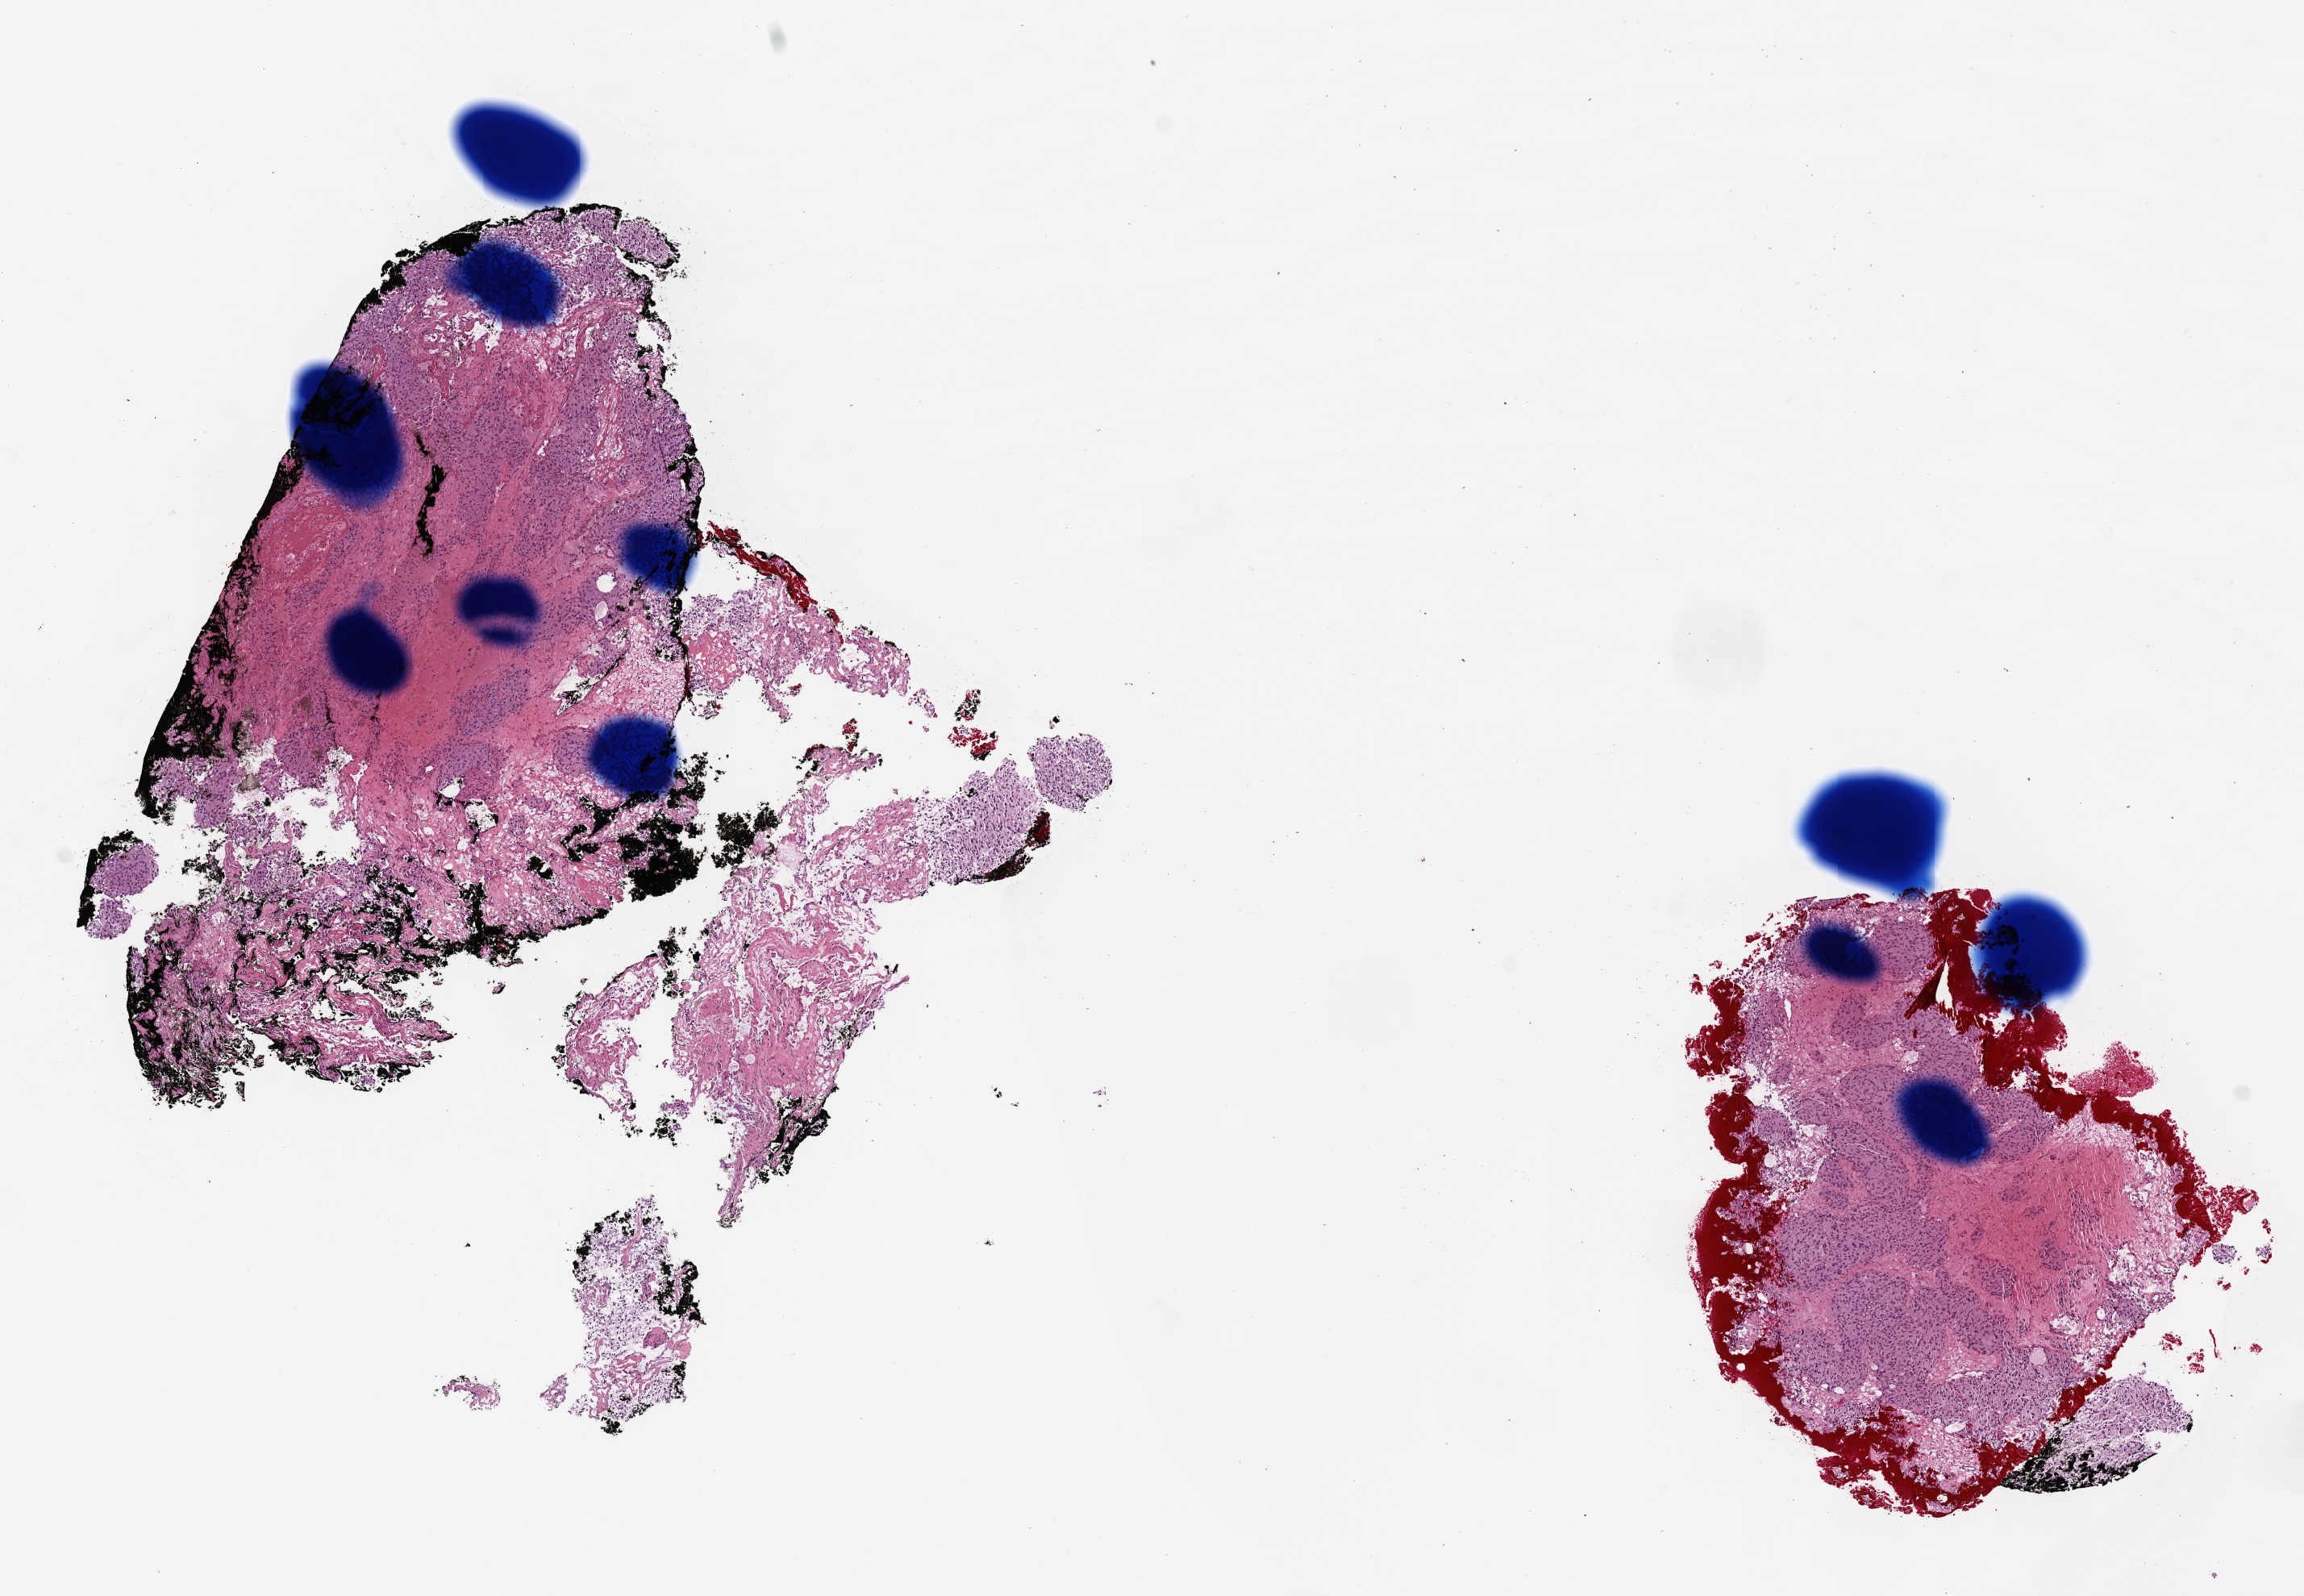
Hematoxylin and eosin (H&E) stained whole-slide image — a low-resolution overview of the entire scanned area, about 11.5 x 8.0 mm (from a 20x scan). Frozen section from the top of the tissue portion. Sample: additional new primary tumour, adrenal gland. Female patient; age at initial diagnosis 21 years. Slide review estimates, as recorded: tumour cells 50%, tumour nuclei 80%, normal cells 0%, stromal cells 50%, necrosis 0%. Inflammatory infiltration, as recorded: lymphocyte infiltration 0%, monocyte infiltration 0%, neutrophil infiltration 0%.
• this section: additional new primary tumour
• patient diagnosis: Pheochromocytoma, malignant